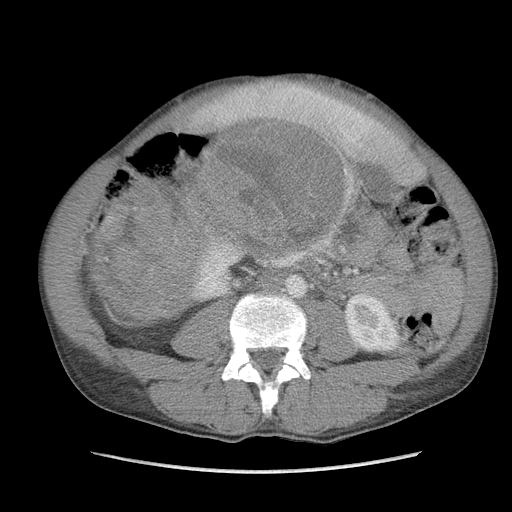
Contrast-enhanced abdominal CT, one axial slice. Position 45 of 115 along the scan axis. Soft-tissue window (W 400 / L 40 HU). 5 mm slice thickness. 512 × 512 image matrix, field of view 360 × 360 mm. Male patient. Case-level facts recorded for this patient, not image findings: diagnosis: adrenocortical carcinoma; tumour side: right adrenal; Ki-67 index: 13 %; stage (as recorded): 3.
Structures marked on this image (semi-automatic segmentation, software-assisted and operator-edited):
- mass: box from (x=99, y=122) to (x=337, y=325) px